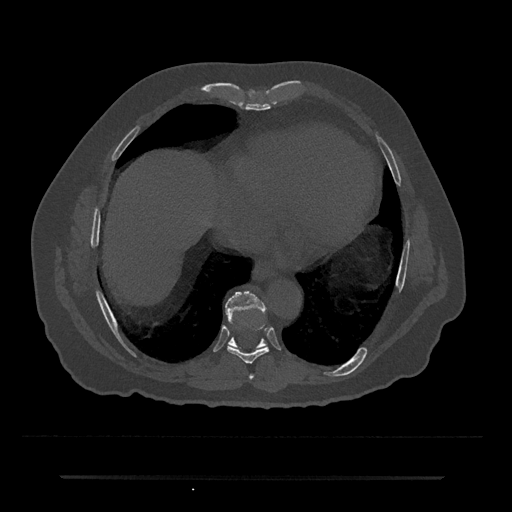
CT including the spine, one axial slice; slice 314 of 797 in the series (ordered by position); bone window (W 1800 / L 400 HU); 0.5 mm slice thickness; 512 × 512 image matrix. Patient: male, 69 years. Case-level facts recorded for this patient, not image findings: primary cancer: prostate.
Outlined on this slice (semi-automatically segmented with operator editing):
- T7 vertebra: bounding box (x1, y1, x2, y2) in pixels: (249, 374, 254, 379)
- T8 vertebra: (227, 325, 269, 364)
- T9 vertebra: (225, 291, 267, 346)